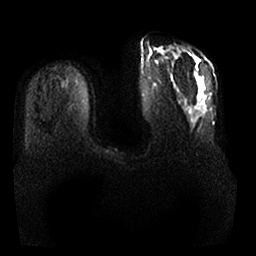
Breast MRI, one axial slice; slice 4 of 25 in the series (ordered by position); diffusion-weighted series; image 2 of 4 stored at this slice position (different b-values; order by instance number); 1.5 T; 4 mm slice thickness; 256 × 256 image matrix, field of view 380 × 380 mm. Female patient.
Structures marked on this image (manually delineated by an expert):
- tumour on diffusion-weighted imaging: box from (x=199, y=80) to (x=204, y=89) px